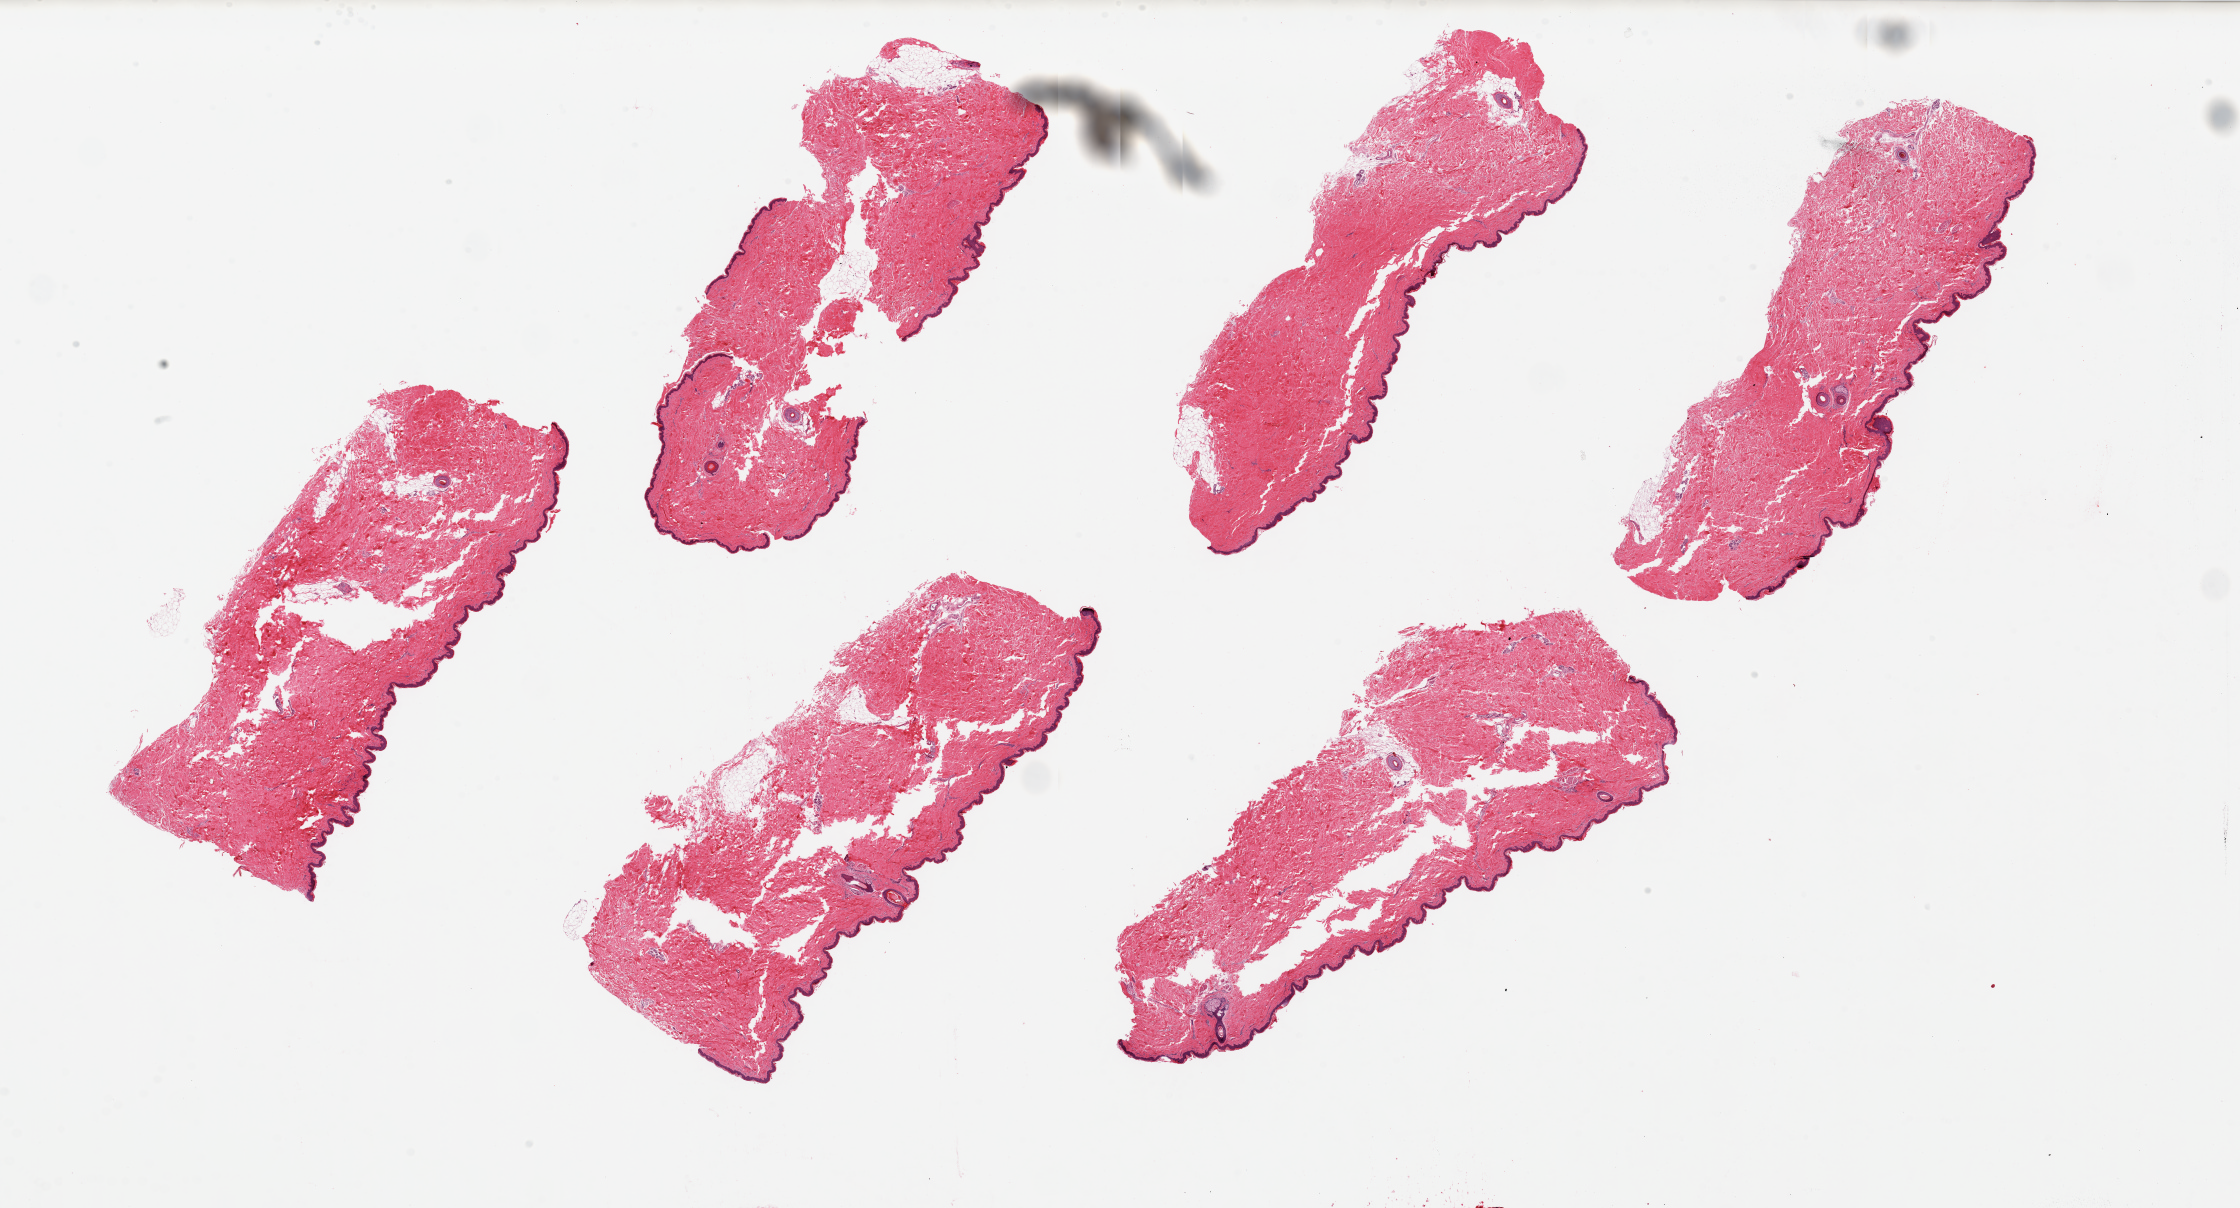
H&E whole-slide image, a low-resolution overview of the entire scanned area, about 35.4 x 19.1 mm (slide scanned at 20x). PAXgene-fixed paraffin-embedded (PFPE) section. Target tissue: skin of suprapubic region. Tissue donor sample. Male donor.
Pathologist's review note for this sample: 6 ~9x3mm pieces, squmaous epithelium is ~1-2% thickness.